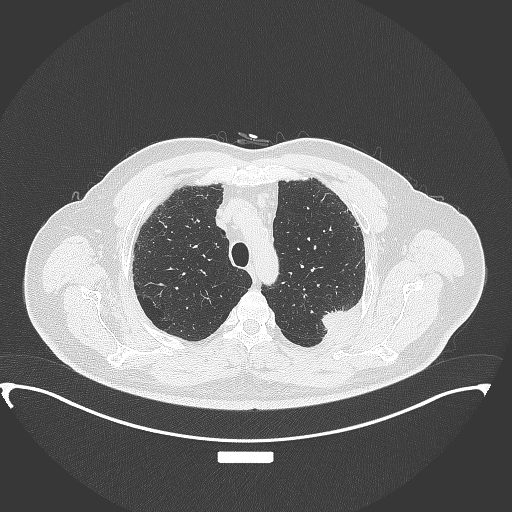
Chest CT, one axial slice. Slice 286 of 350 in the series (ordered by position). Reconstruction kernel B70f. 120 kVp. Lung window (W 1500 / L -600 HU). 1 mm slice thickness. 512 × 512 image matrix, field of view 459 × 459 mm. Male patient, age 64 years. From the clinical record (not read from this slice): clinical TNM (as recorded): T1c N1 M1.
Outlined on this slice (rectangle marked by the reading radiologist):
- lung tumour (recorded histology: adenocarcinoma): box from (x=318, y=307) to (x=362, y=337) px